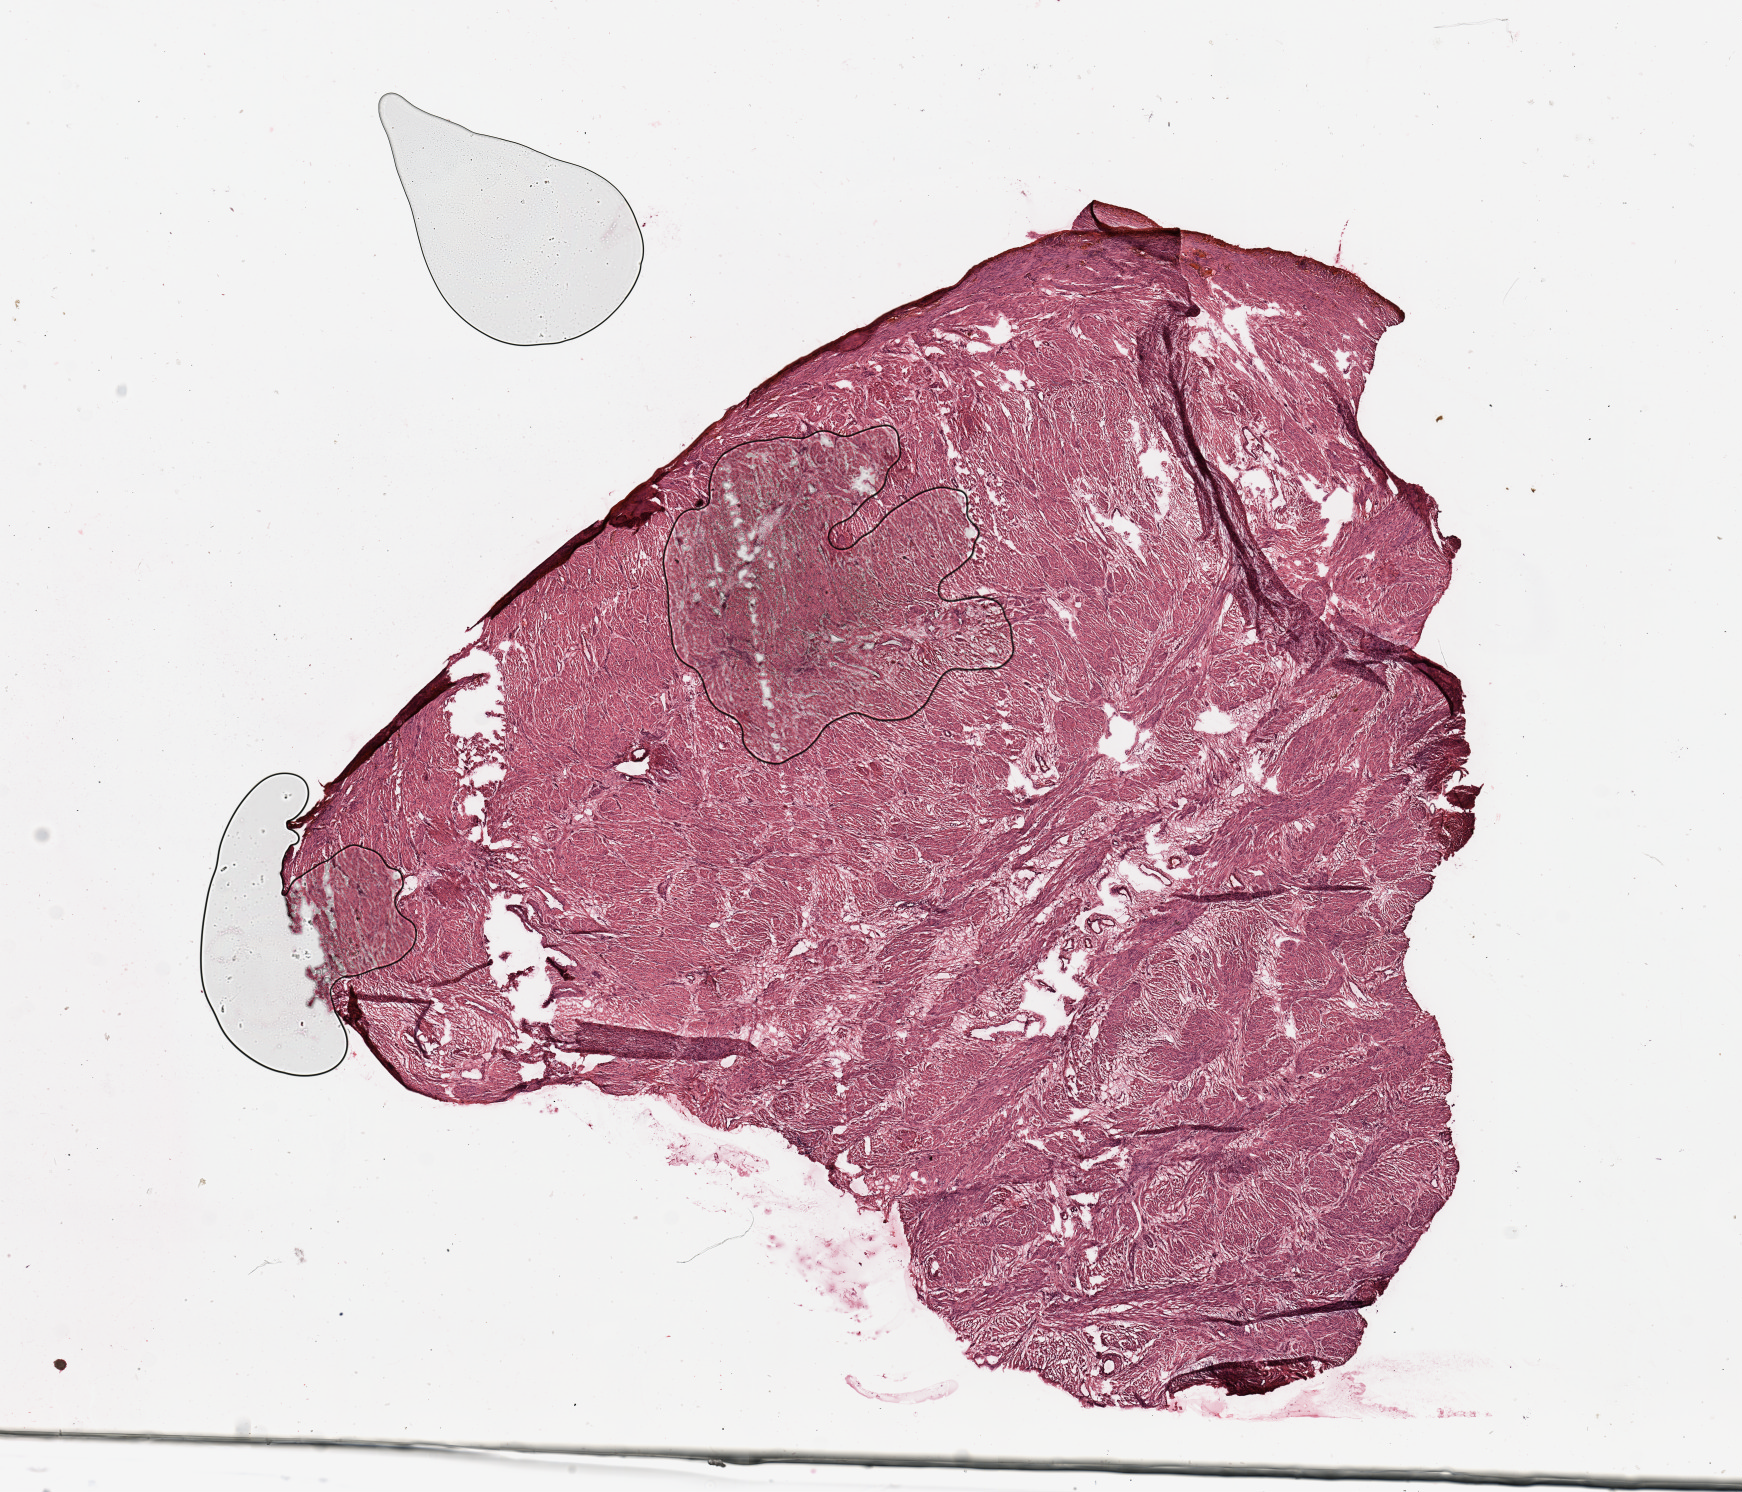
Whole-slide histology image, H&E-stained — low-resolution overview of the scanned area, about 13.8 x 11.8 mm (slide scanned at 20x). Normal (non-tumour) tissue sample, uterus. 45-year-old female patient.
* this section: normal (non-tumour) tissue from the same patient
* patient diagnosis: Endometrioid adenocarcinoma, NOS